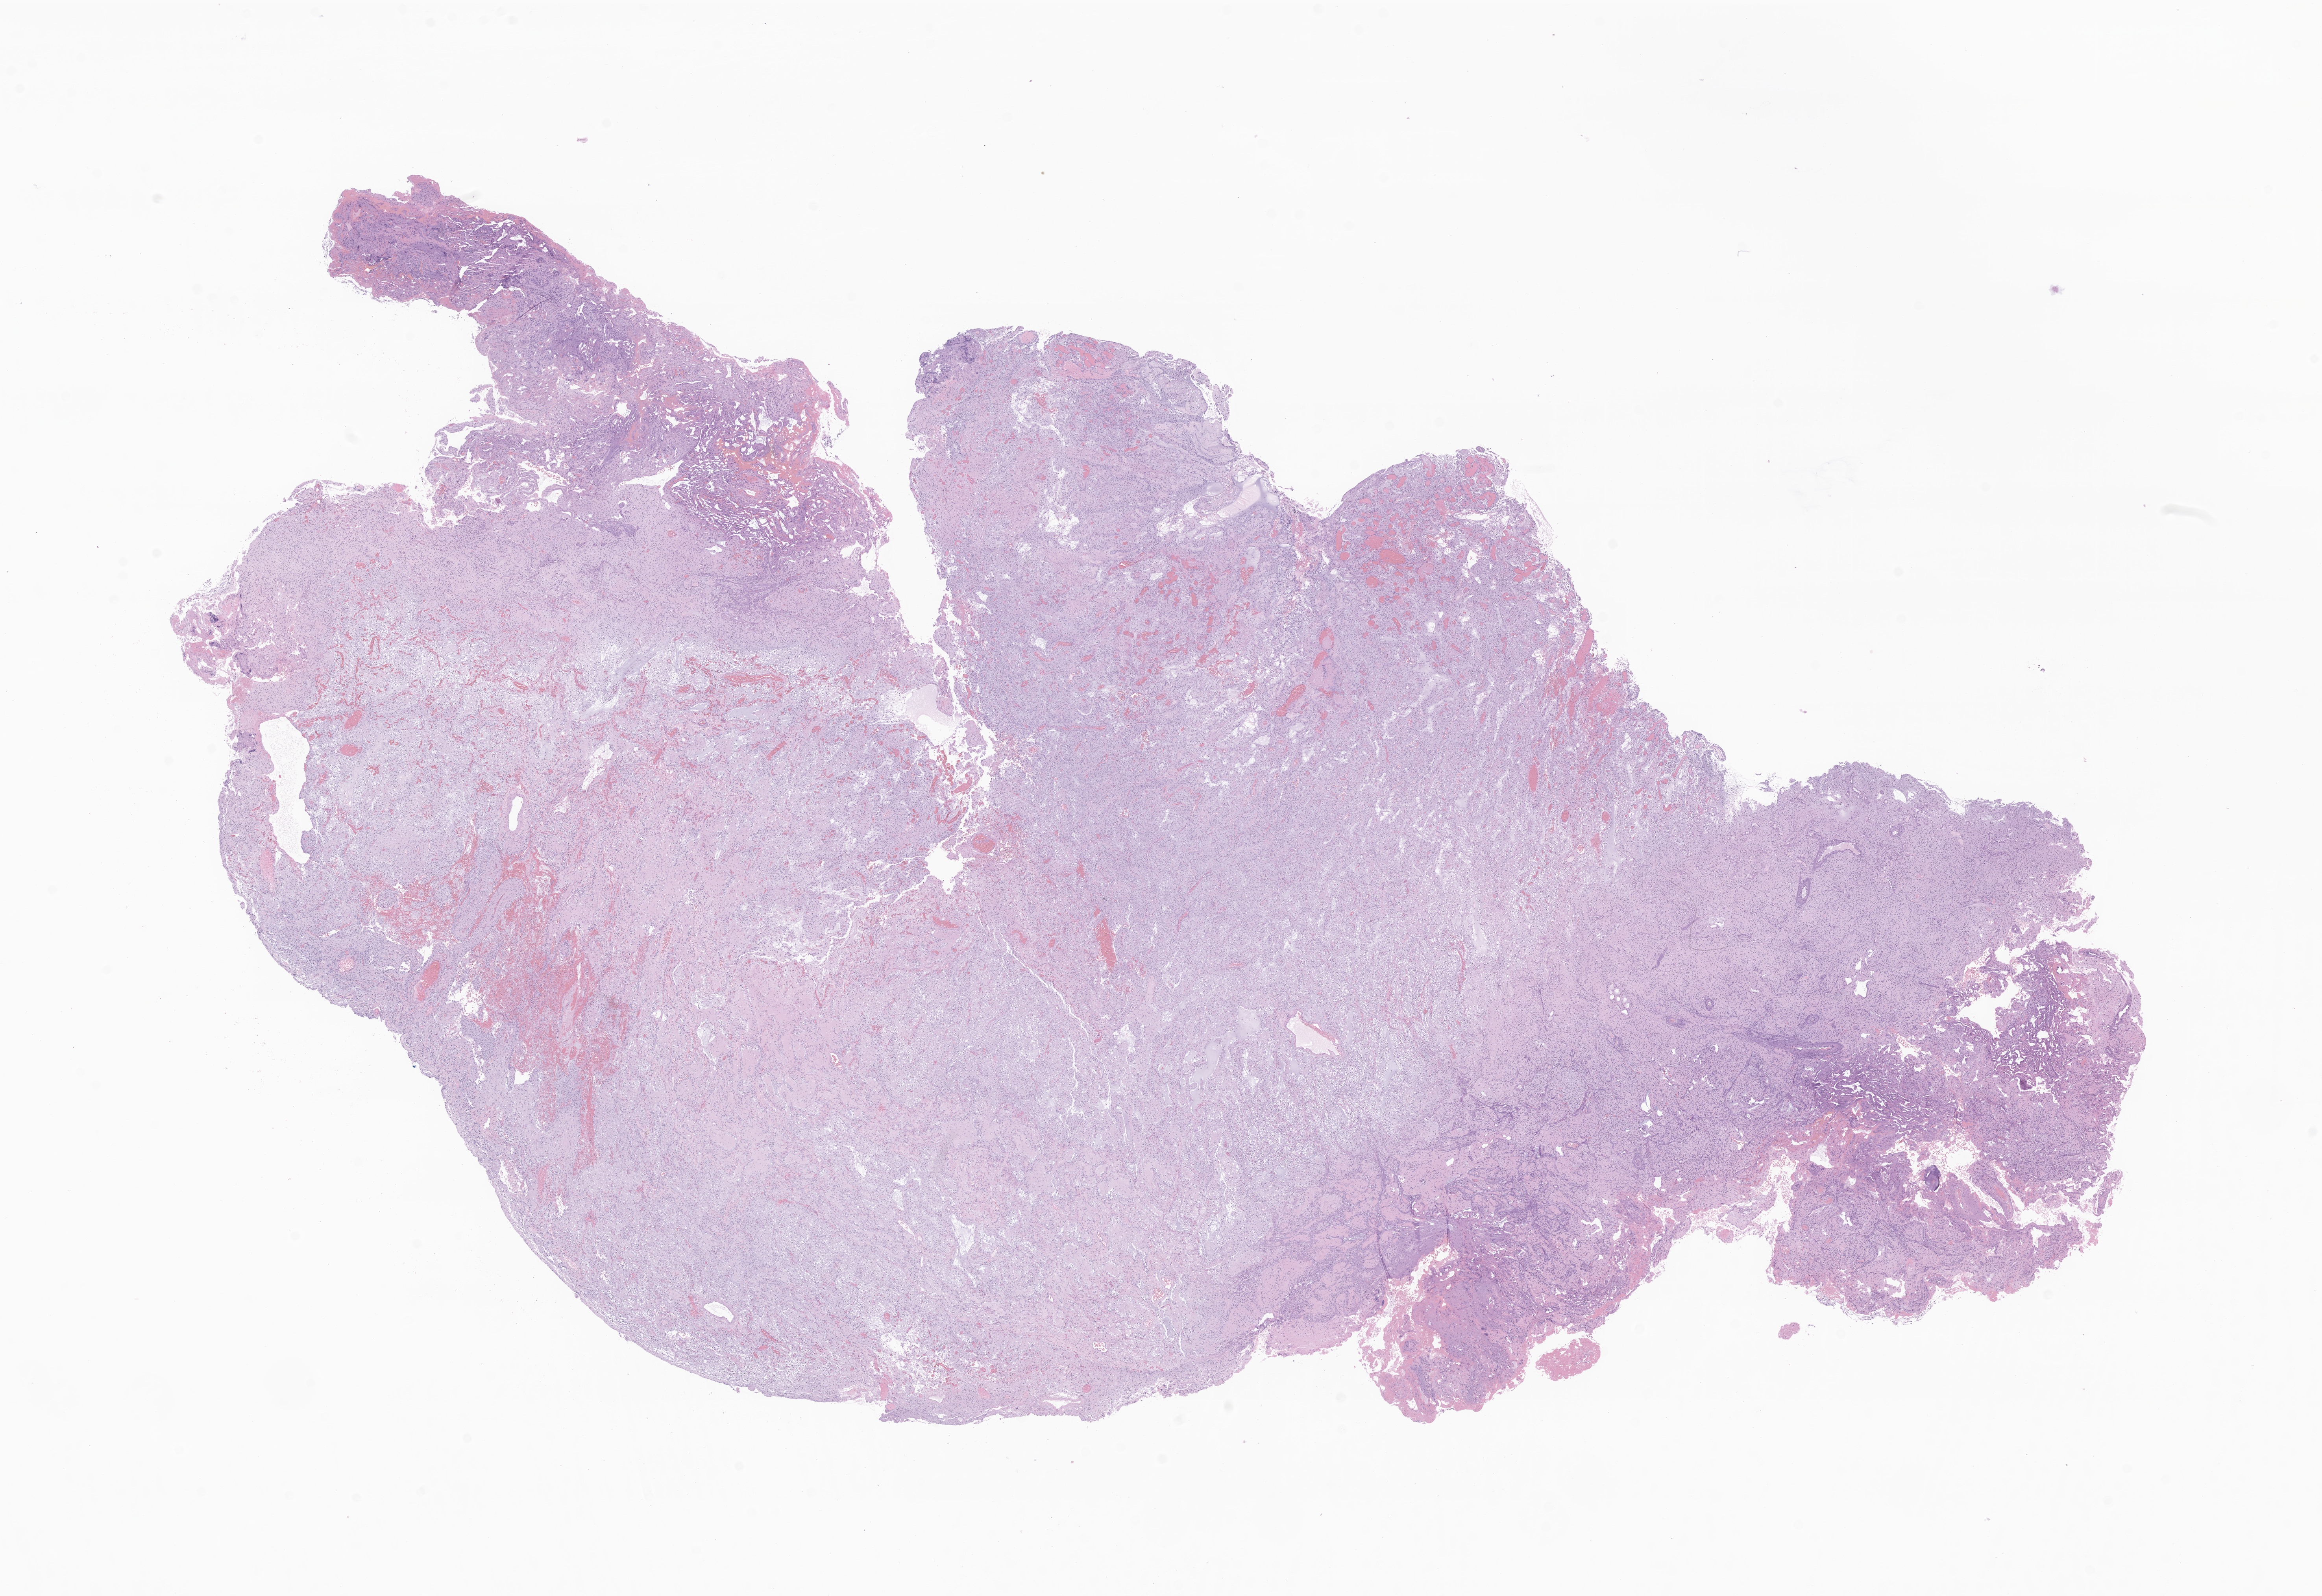
H&E whole-slide image of tumor tissue from the brain — shown as a low-resolution overview of the whole scanned area (about 24.9 x 17.1 mm), formalin-fixed, paraffin-embedded (FFPE) tissue. Patient male; age 77 months (6 years 5 months).
Diagnosis (ICD-O-3 morphology term): Tumor cells, uncertain whether benign or malignant.